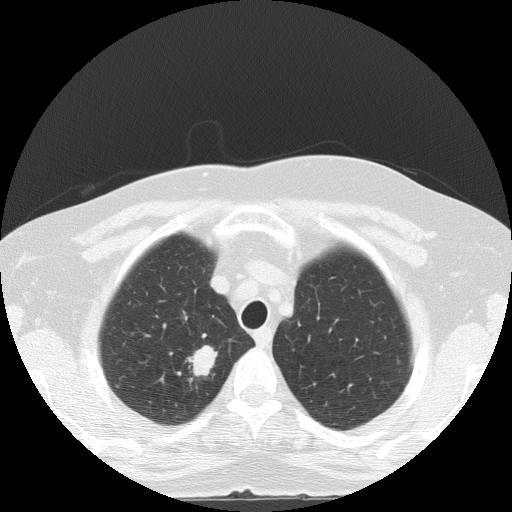
Axial slice from a low-dose chest CT screening exam. Baseline annual screen. Lung window (W 1500 / L -600 HU). 2 mm slice thickness. Lung (sharp) reconstruction kernel (FC51). 512 × 512 image matrix, field of view 320 × 320 mm. Female, age 56 years at enrolment. Current smoker at enrolment.
Lesion marked by an expert reader, bounding box [x1, y1, x2, y2] px = [171, 339, 233, 389]. The screening reader recorded 2 non-calcified nodules or masses ≥4 mm on this exam (right upper lobe, right lower lobe); which of them this box marks is not recorded. Official screen result: positive, change unspecified: nodule(s) >= 4 mm or enlarging nodule(s), mass(es), or other non-specific abnormalities suspicious for lung cancer. Participant outcome: lung cancer diagnosed 24 days after this screen — adenocarcinoma, NOS, right upper lobe, poorly differentiated (G3), stage IA (AJCC 6th edition), 20 mm at pathology.